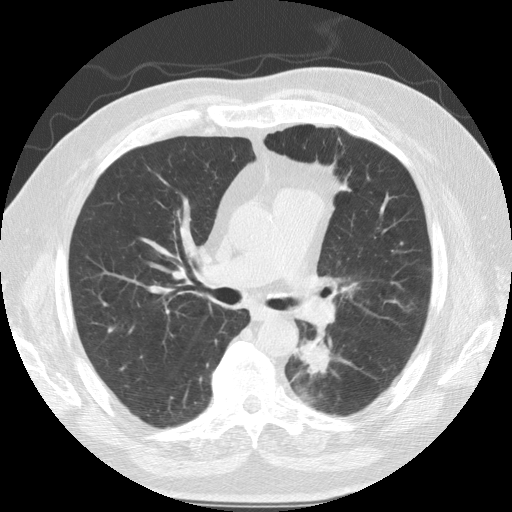
Low-dose screening chest CT, axial slice, first (baseline) screen, lung window (W 1500 / L -600 HU), slice 53 of 124 in the series. Male participant, aged 68 years at enrolment. Former smoker at enrolment.
Expert-annotated lung lesion, box from (x=280, y=318) to (x=351, y=396) px. The screening reader recorded 3 non-calcified nodules or masses ≥4 mm on this exam (left lower lobe, lingula, right lower lobe); which of them this box marks is not recorded. Lung cancer was diagnosed 35 days after this screen: squamous cell carcinoma, NOS, left lower lobe, poorly differentiated (G3), stage IIB (AJCC 6th edition), 40 mm at pathology.